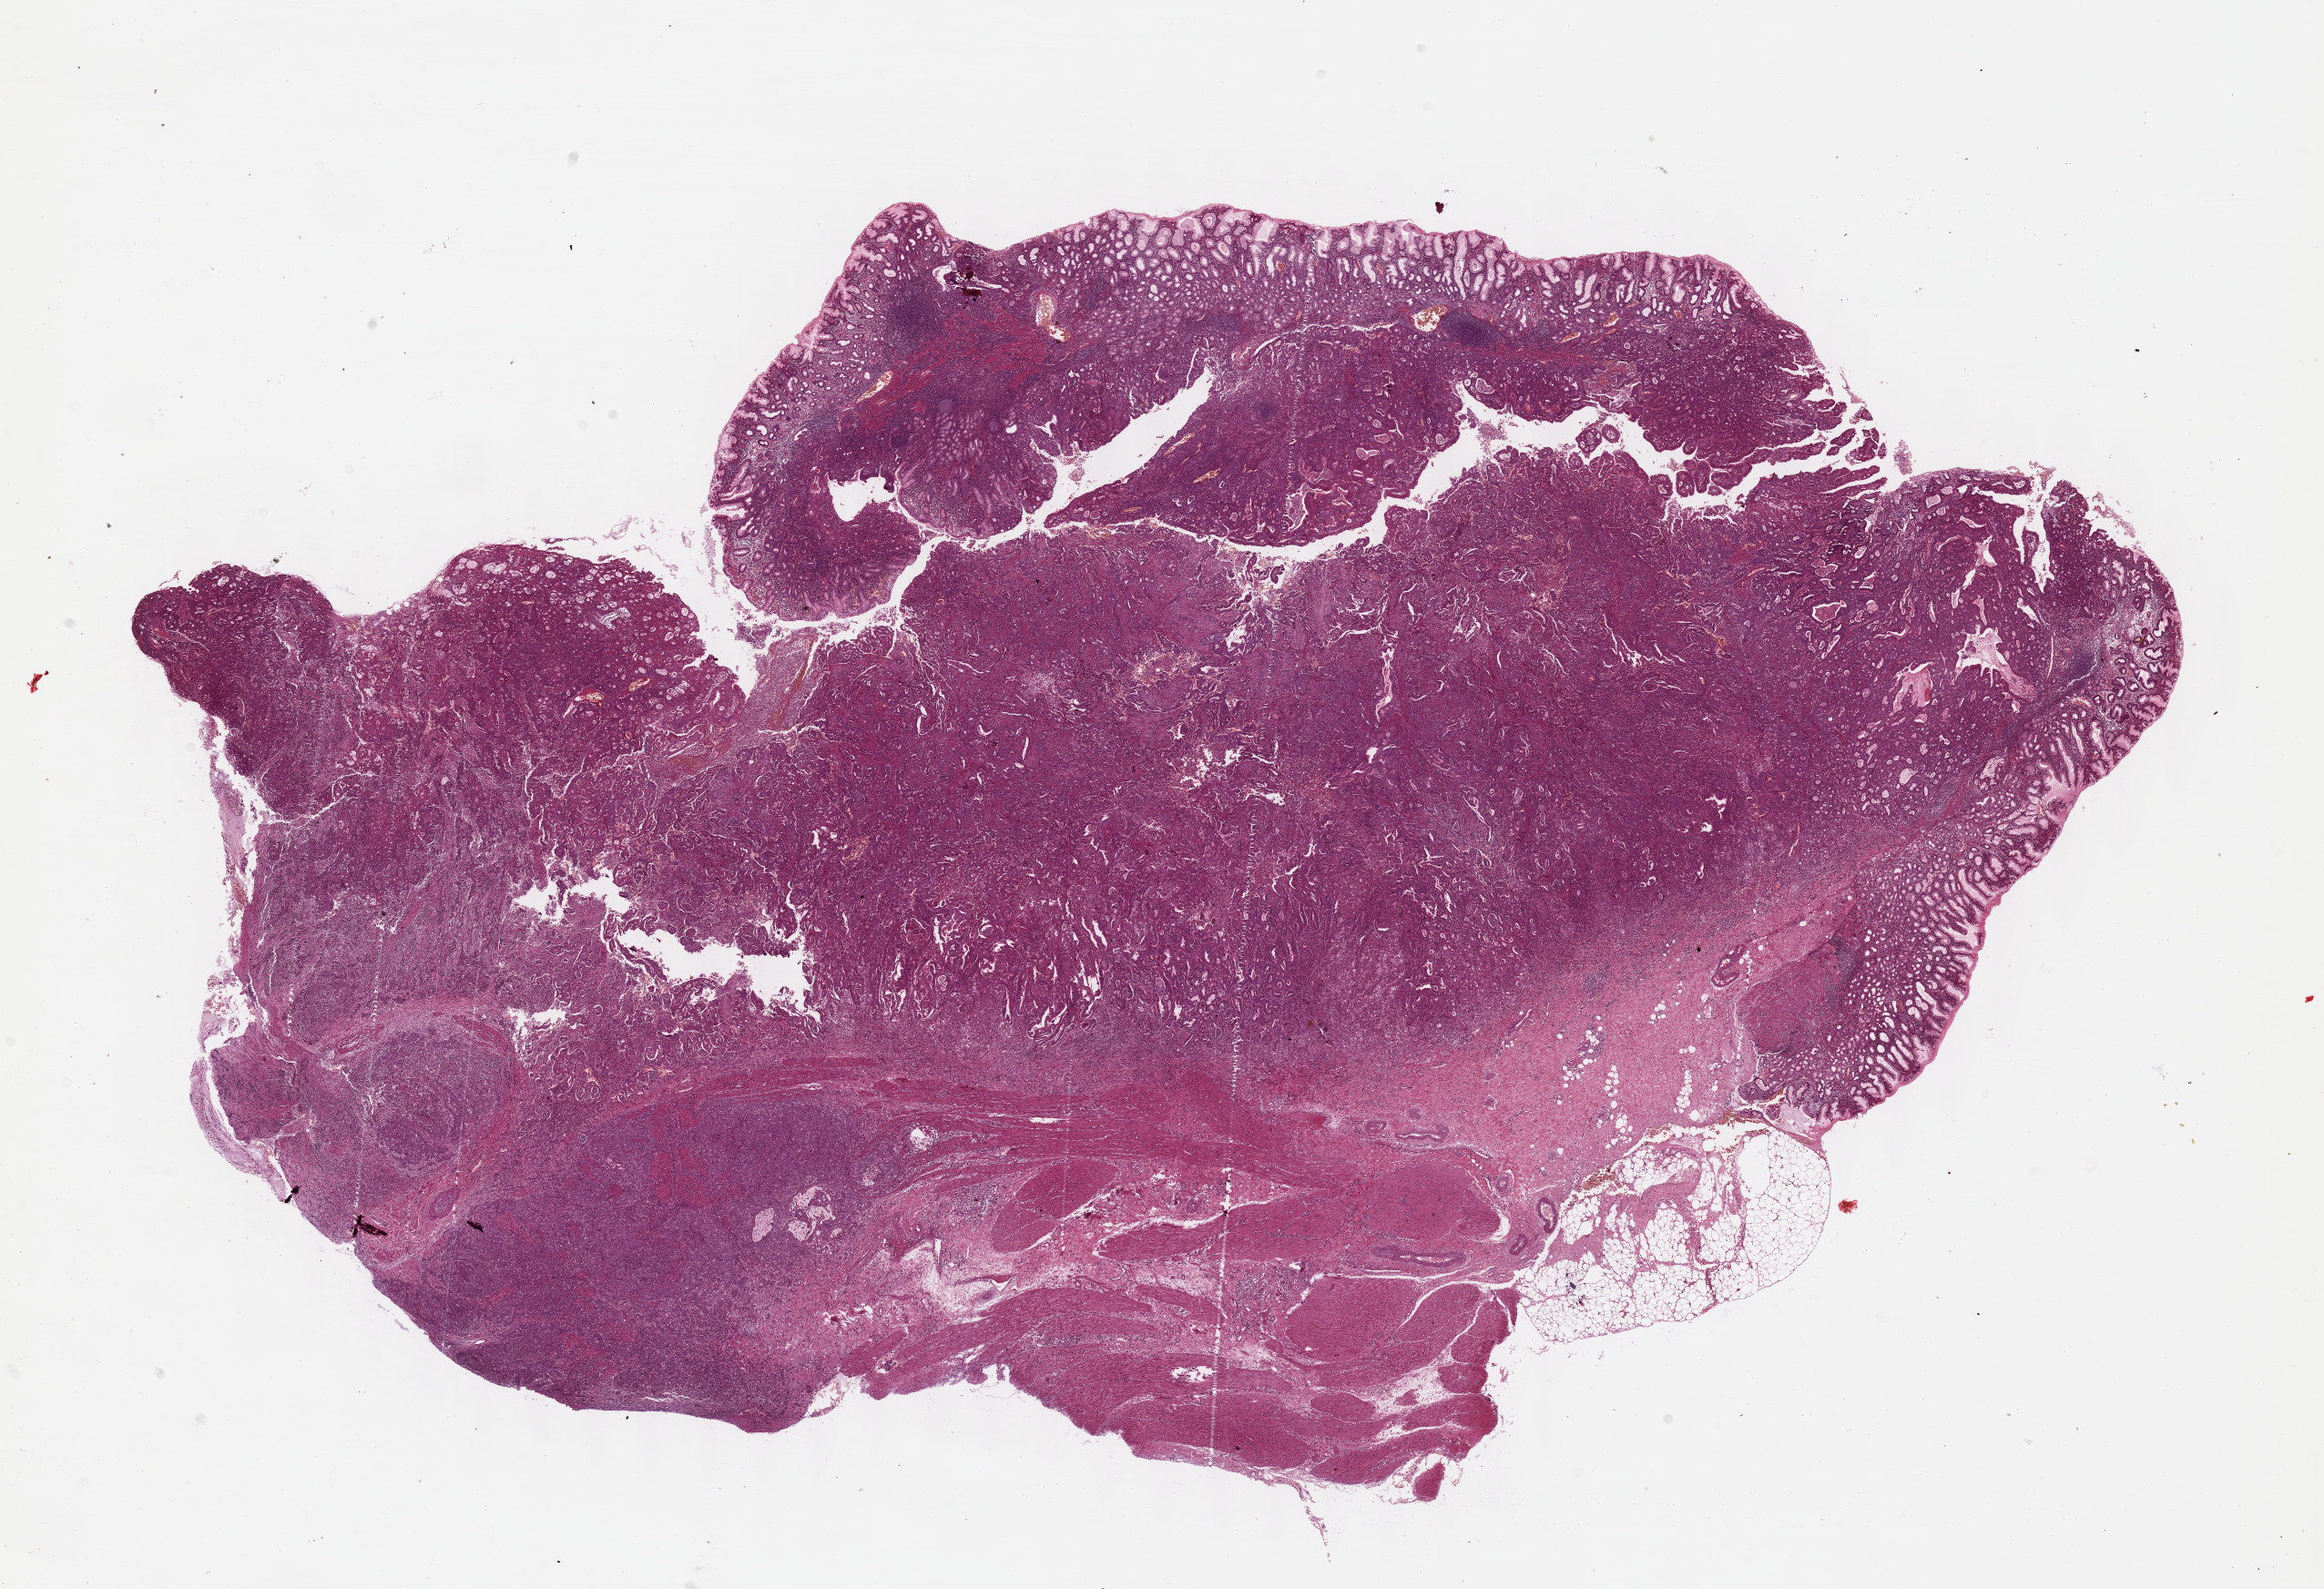
Digitized H&E tissue section (whole slide), low-resolution overview of the scanned area, about 20.6 x 14.1 mm. FFPE section. Primary tumour sample from the stomach. Patient: male, age at initial diagnosis 74 years. Histologic grade: G3 (poorly differentiated).
Histologic diagnosis: Adenocarcinoma, NOS. AJCC pathologic stage: II.